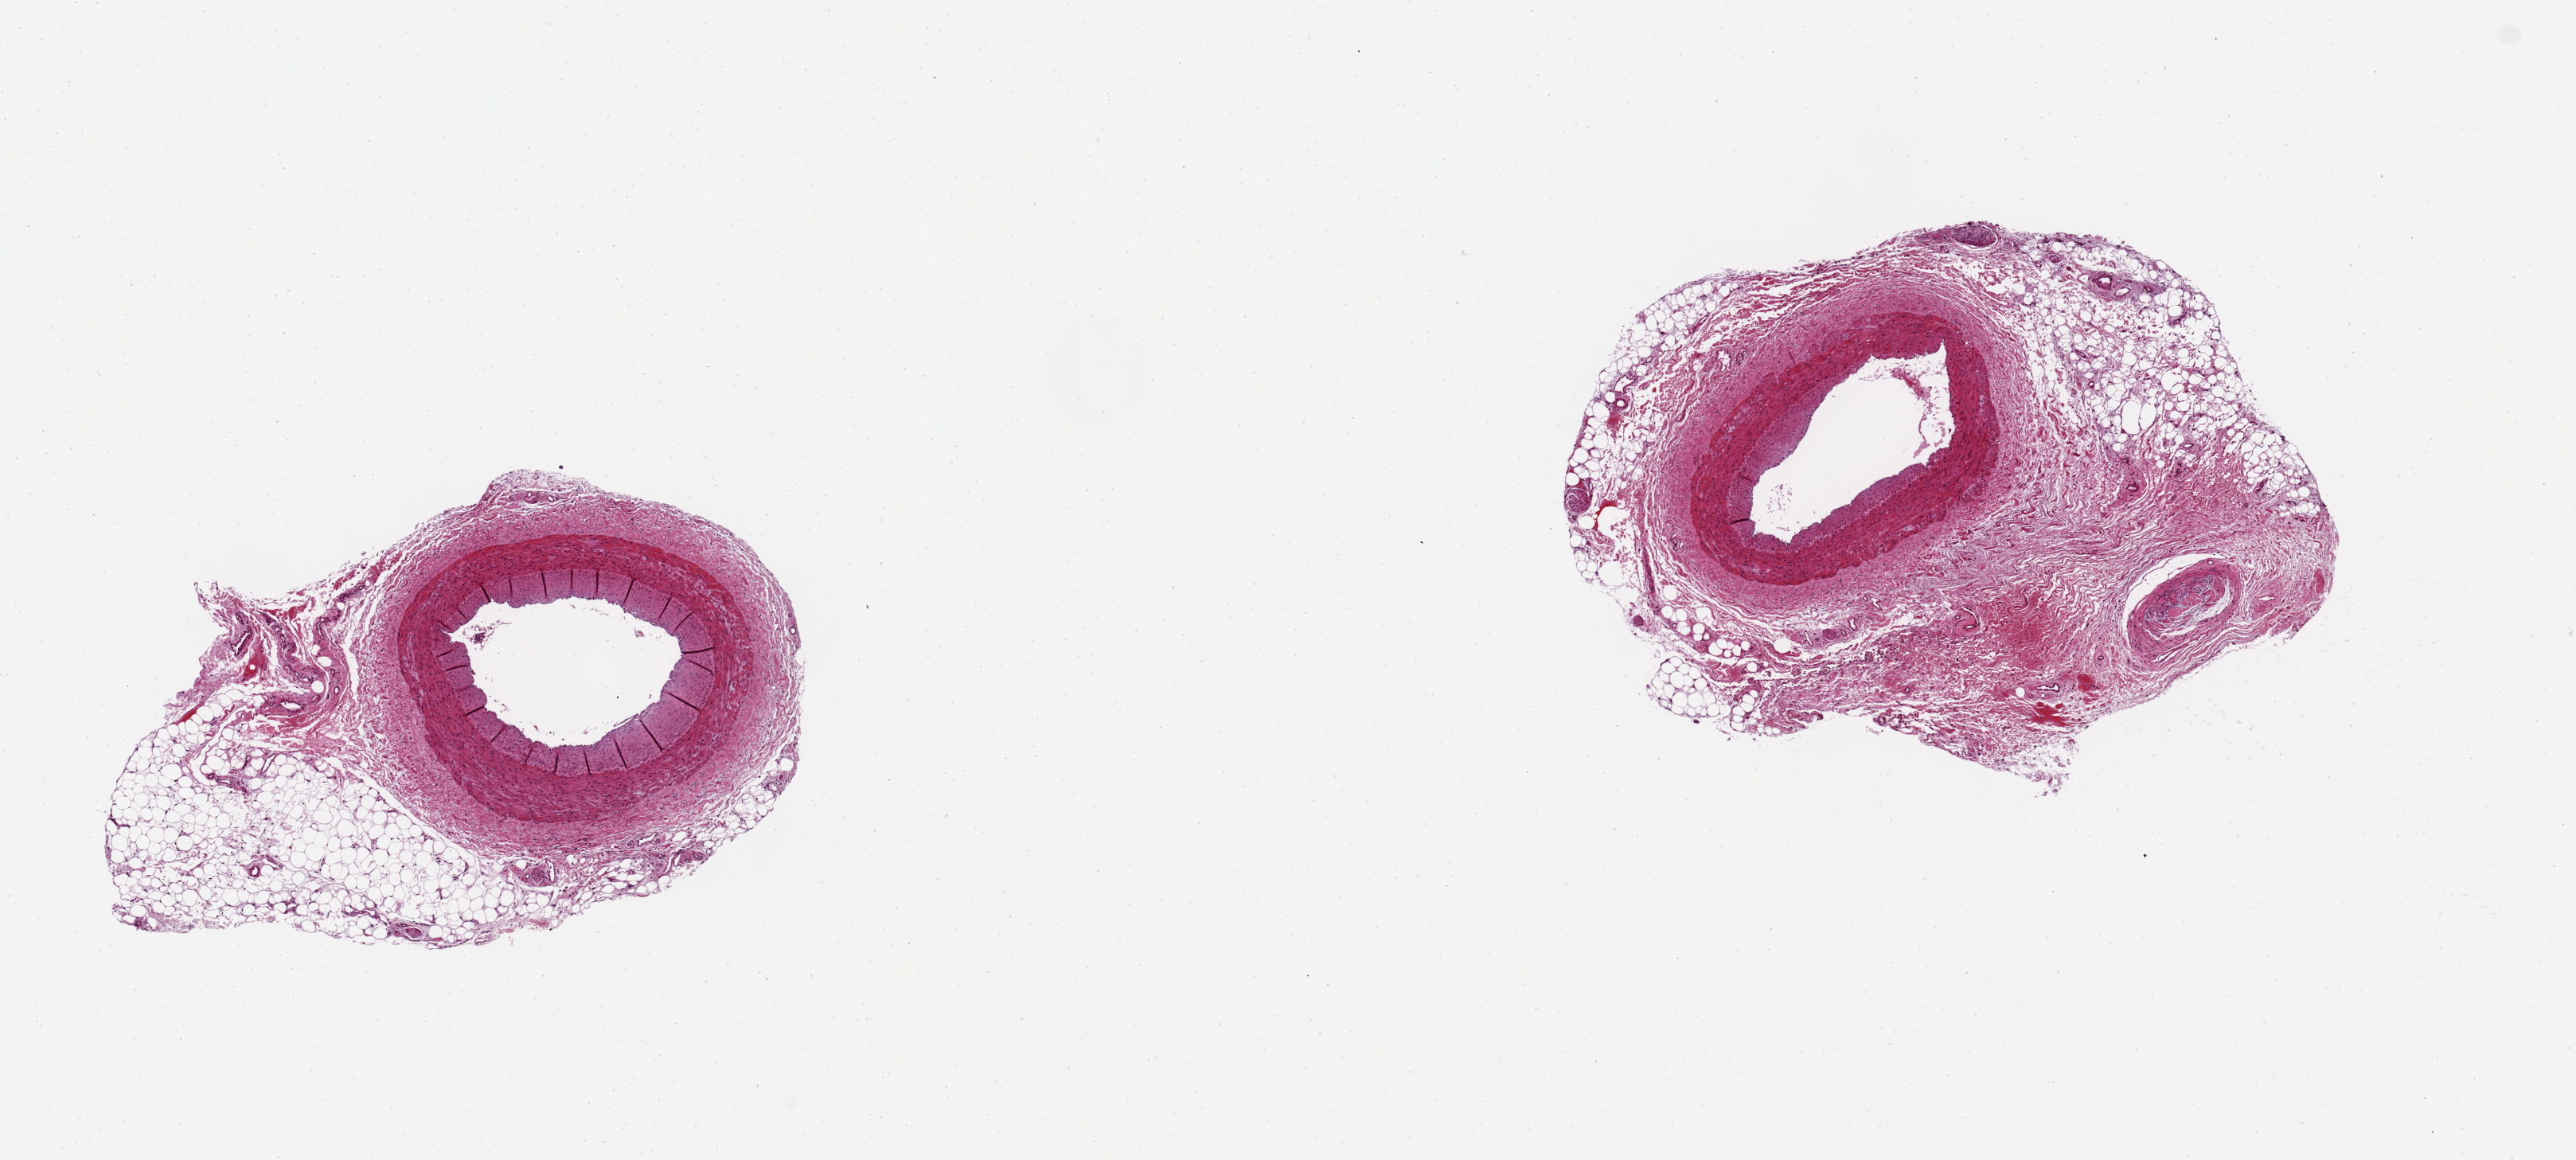
Hematoxylin and eosin (H&E) whole-slide image, brightfield — a low-resolution overview of the entire scanned area, about 12.8 x 5.8 mm. Donor: female.
Specimen: PAXgene-fixed, paraffin-embedded tissue; sampled site (target tissue): coronary artery; donor tissue sample.